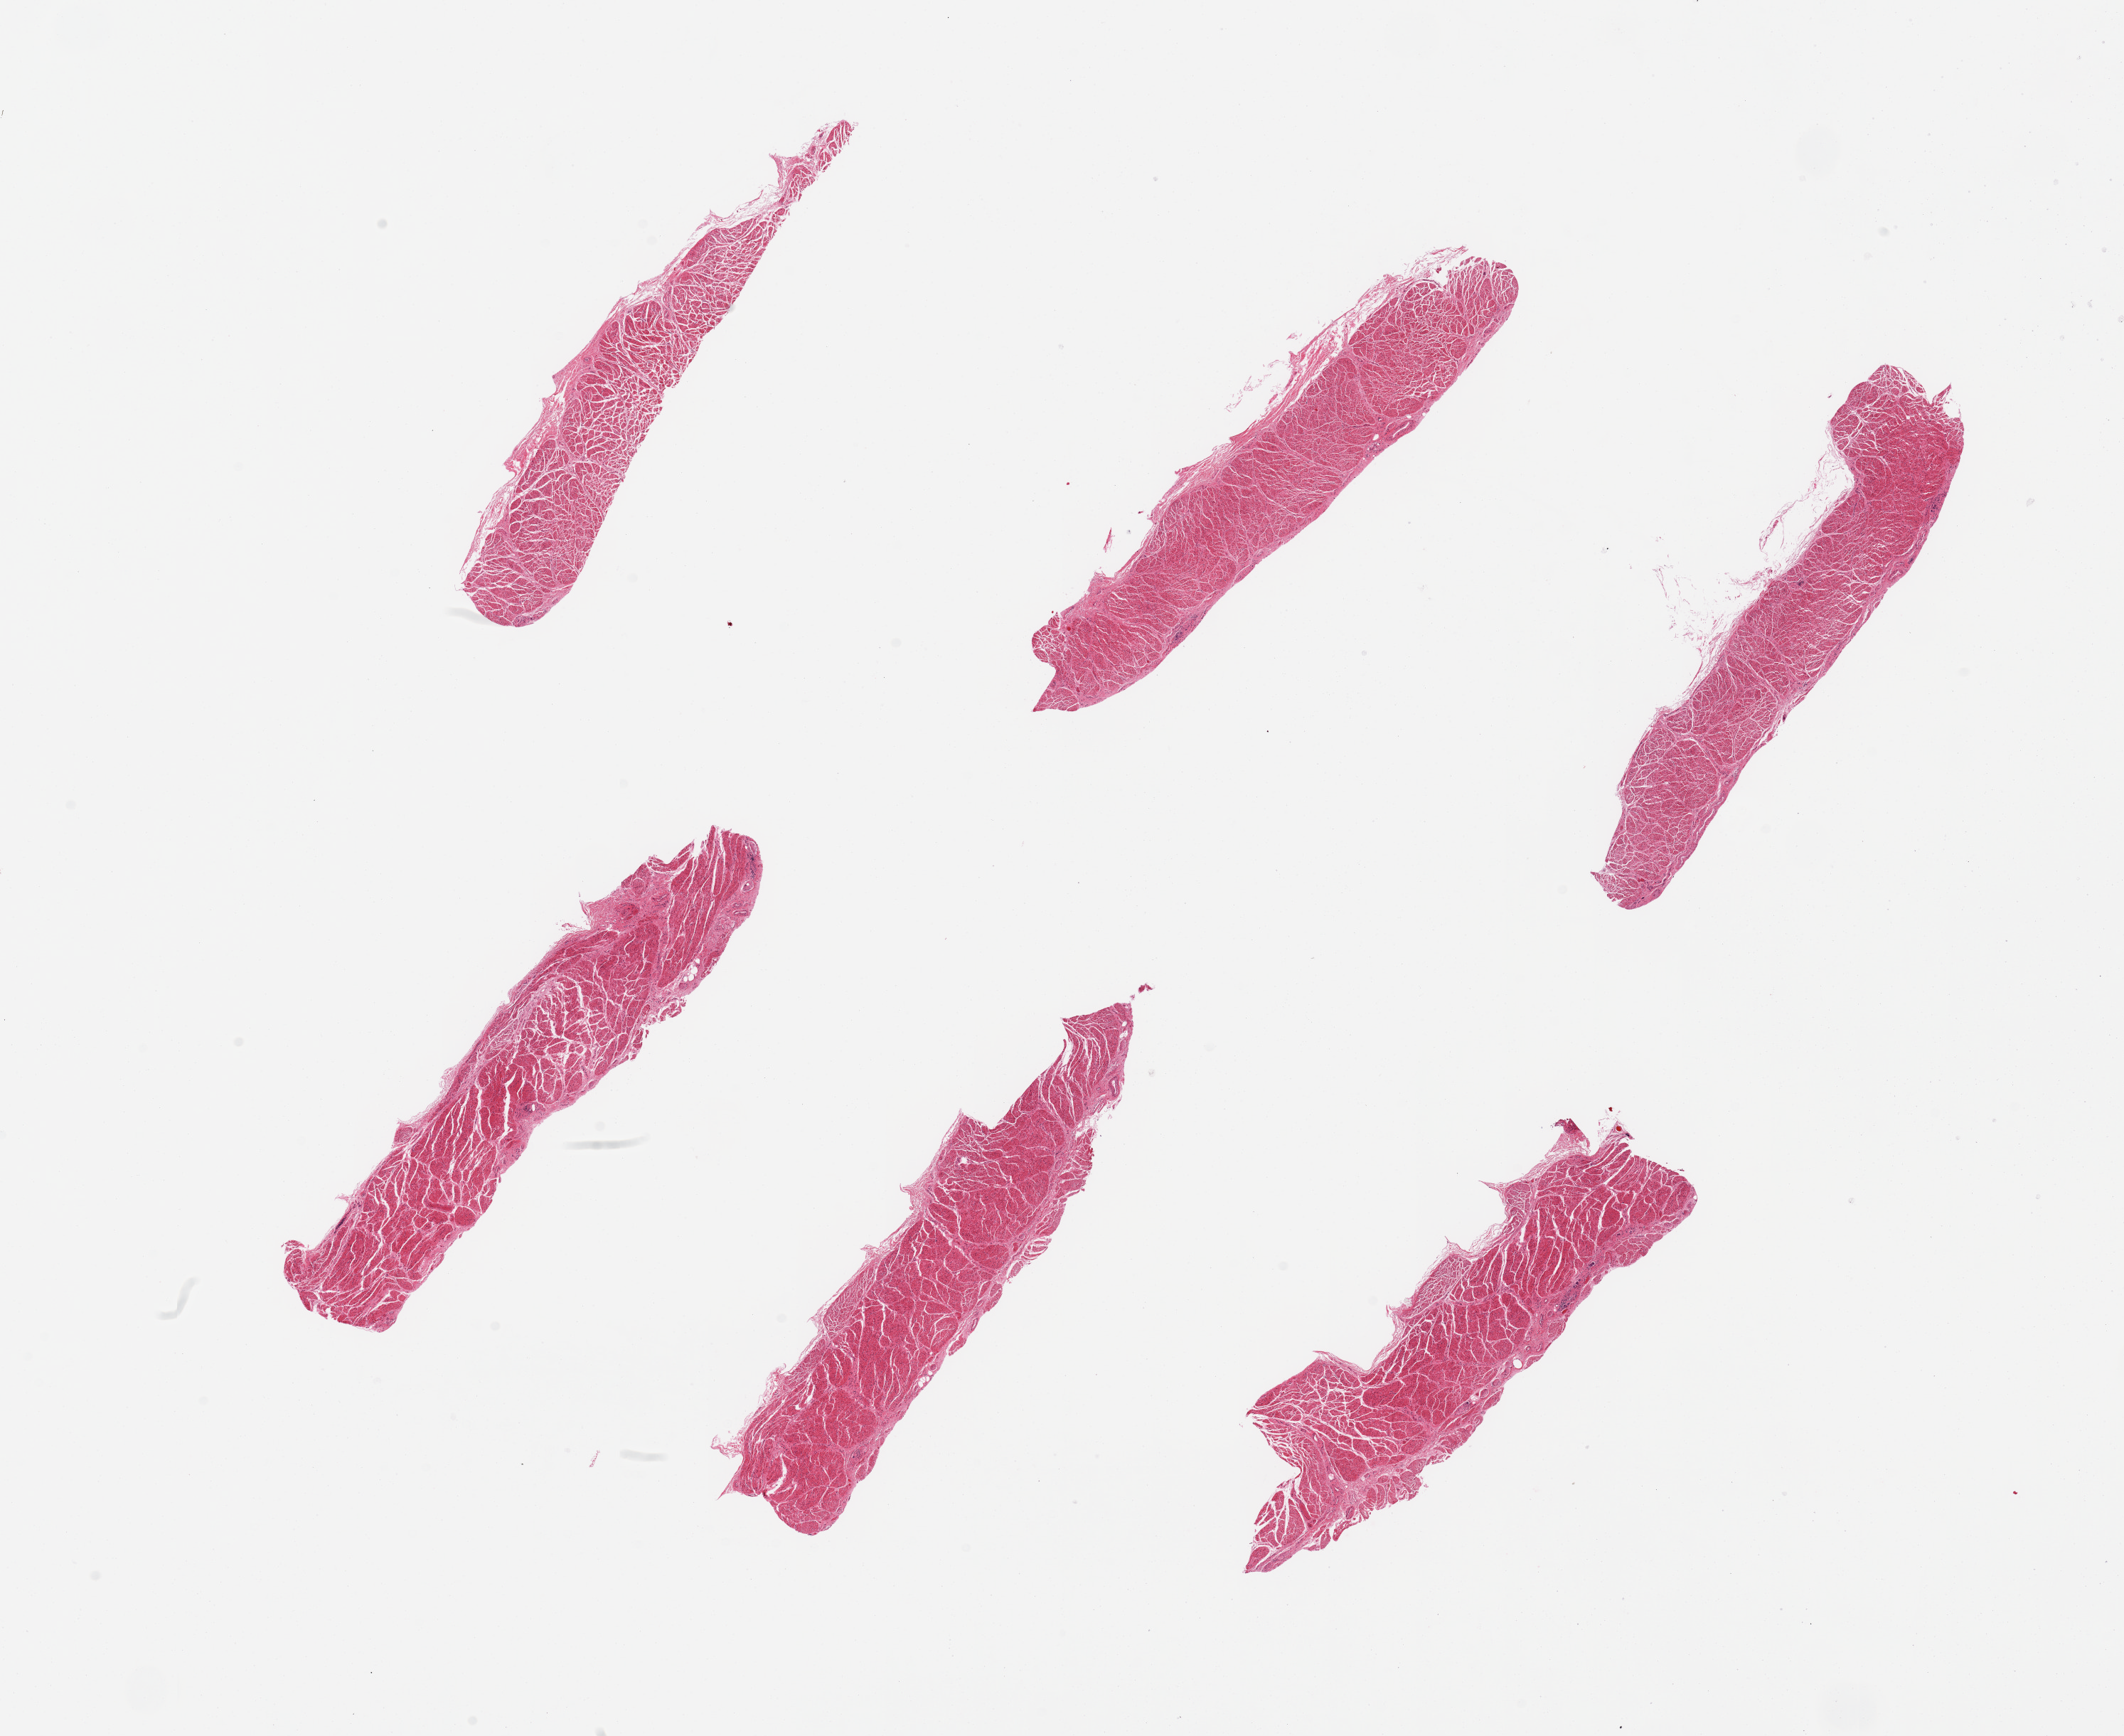
Whole-slide image, hematoxylin and eosin (H&E) stain — shown as a low-resolution overview of the whole scanned area (about 23.6 x 19.3 mm, acquisition: 20x scan), PAXgene-fixed paraffin-embedded (PFPE) section, target tissue: esophageal muscle, donor tissue sample. Donor sex: male.
- pathologist's review note for this sample: 6 pieces; well trimmed muscle